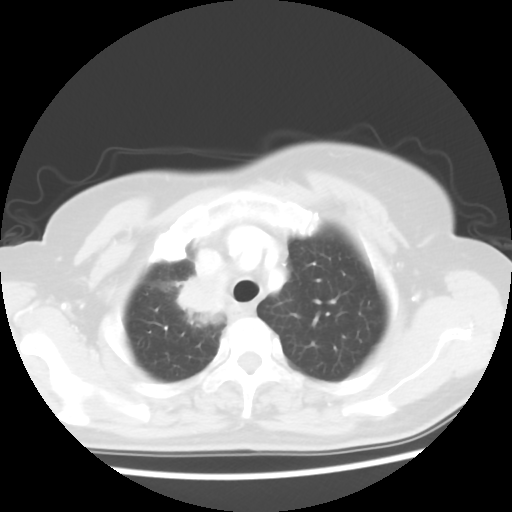
Chest CT, one axial slice. Slice 47 of 56 in the series (ordered by position). Reconstruction kernel STANDARD. Lung window (W 1500 / L -600 HU). 5 mm slice thickness. 512 × 512 image matrix, field of view 314 × 314 mm. Patient: female, 62 years. Case-level facts recorded for this patient, not image findings: clinical TNM (as recorded): T2 N1 M1a.
Outlined on this slice (bounding box drawn by a radiologist):
- lung tumour (recorded histology: adenocarcinoma): bounding box <169,259,227,324> (left, top, right, bottom; pixels)